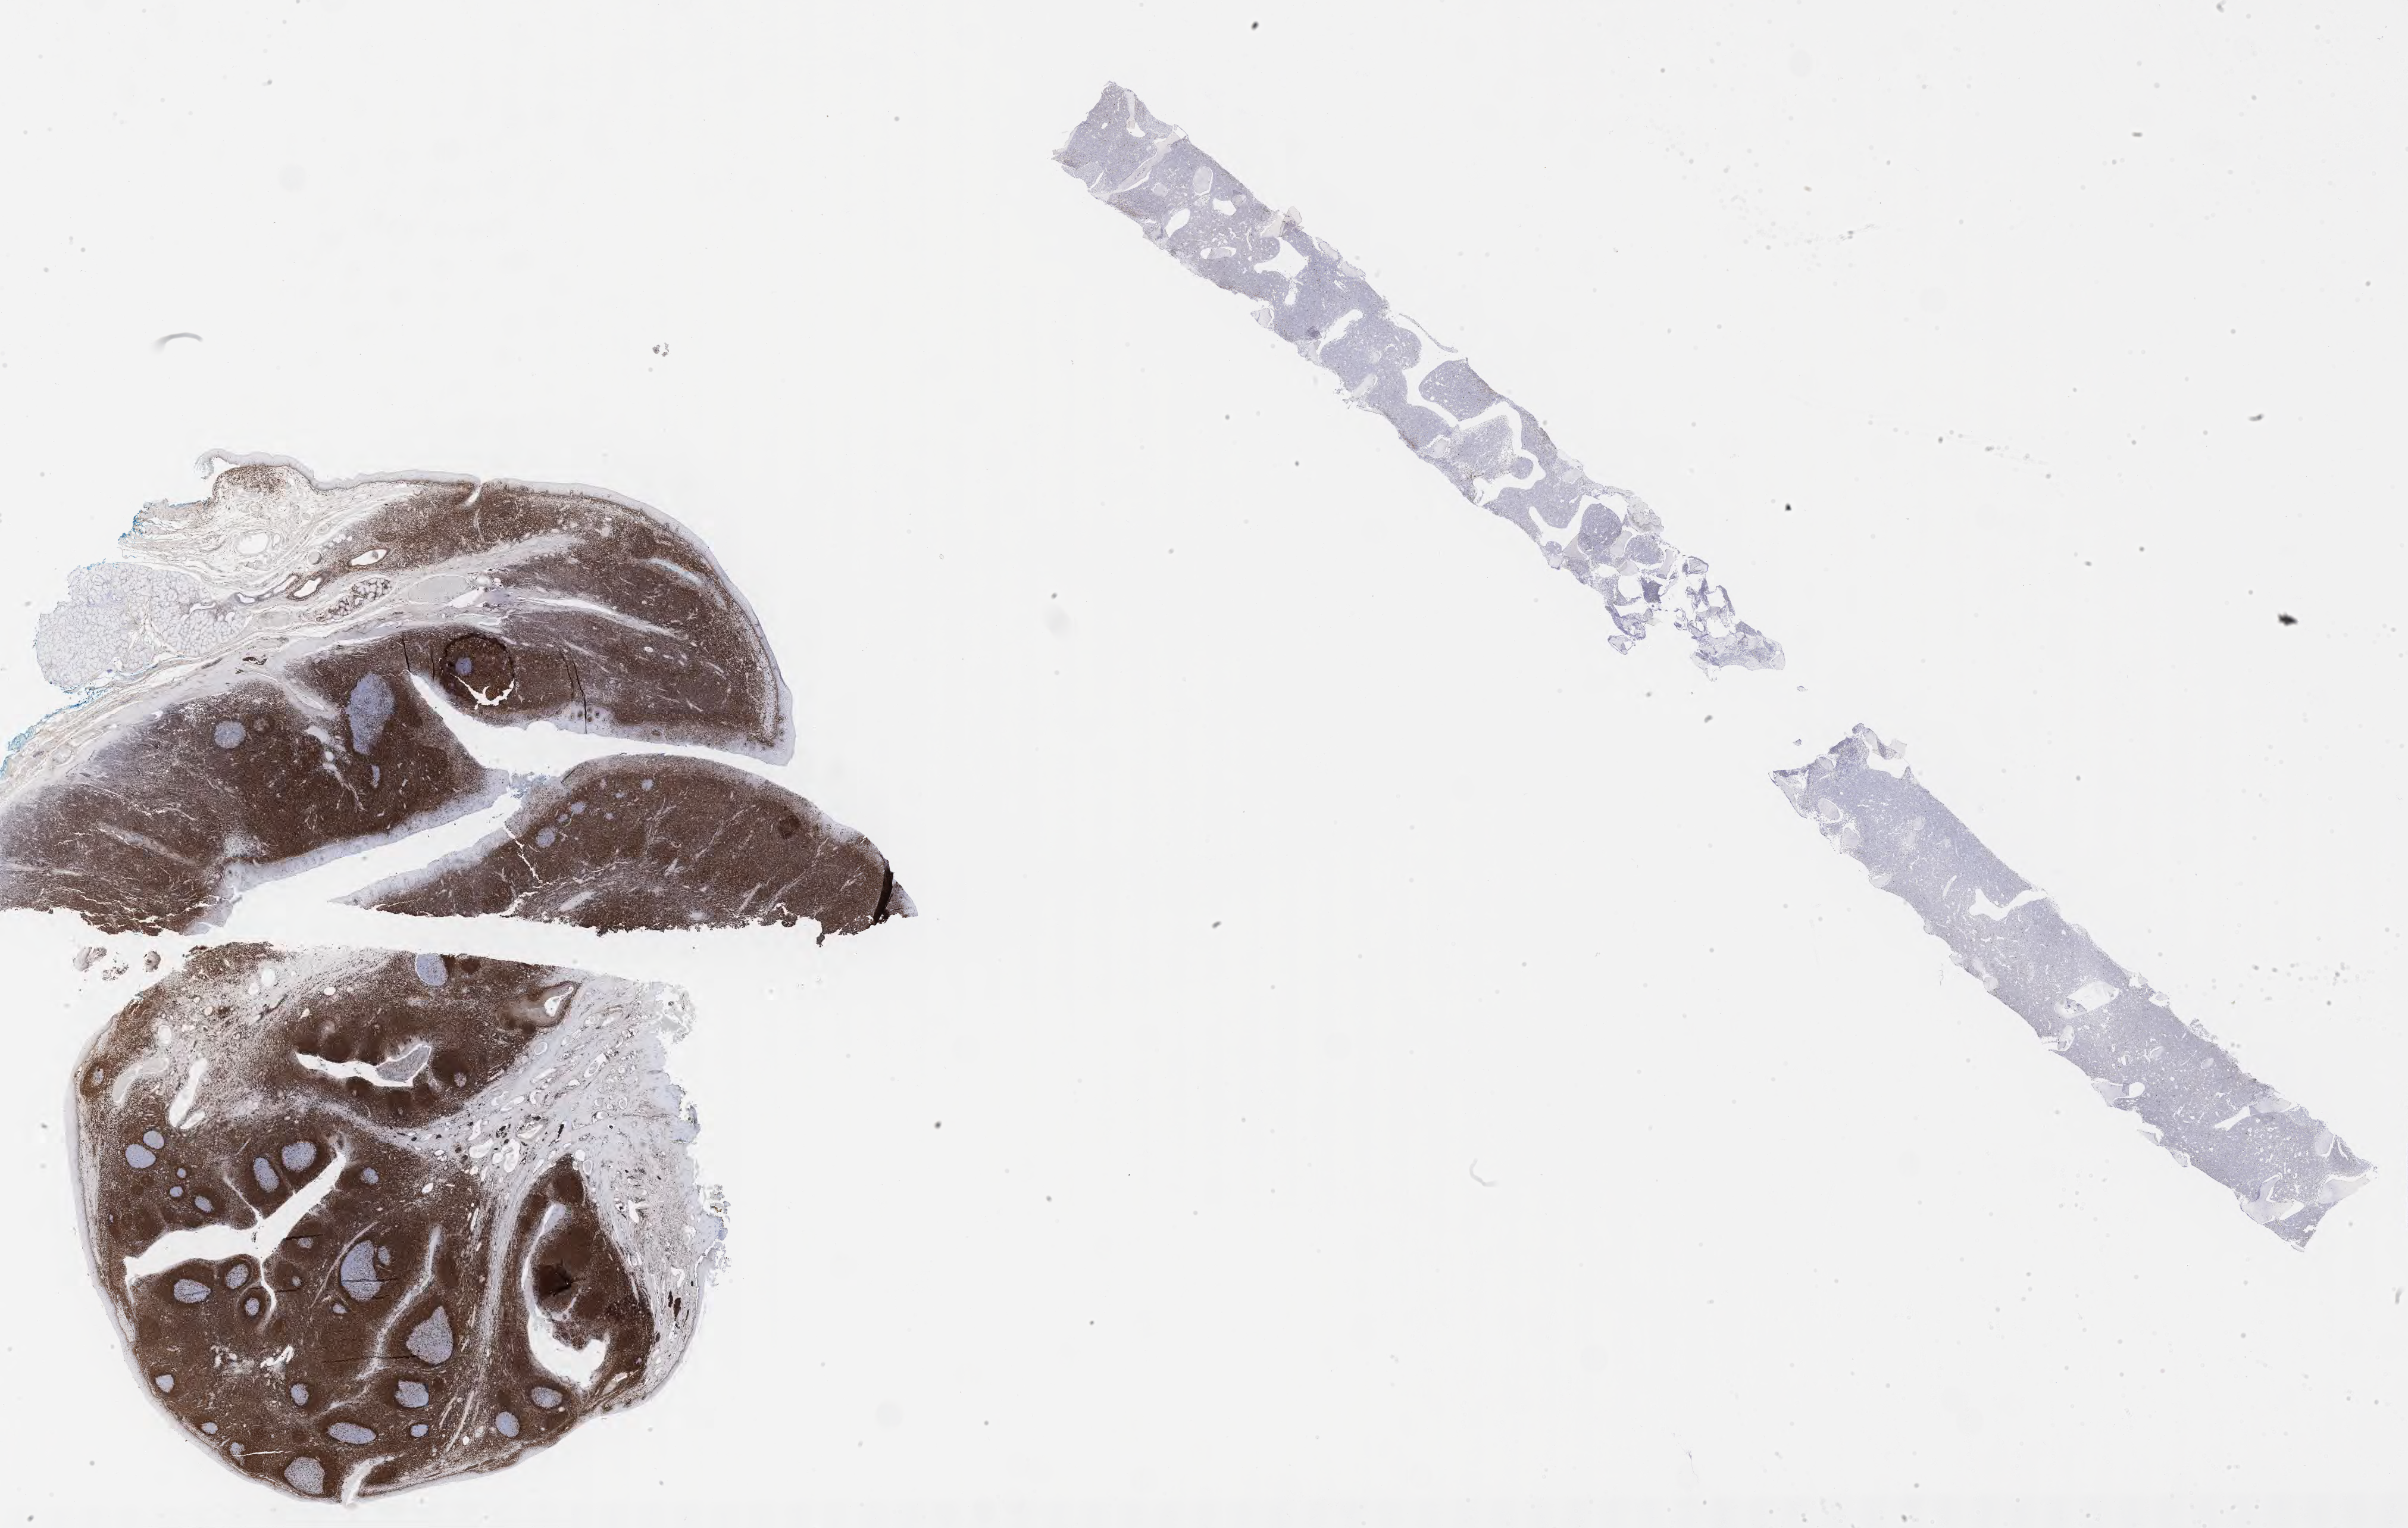
Whole-slide image, immunohistochemical stain for BCL2, shown as a low-resolution overview of the whole scanned area (about 32.7 x 20.8 mm). Tumor tissue. Male, age 7 years at initial diagnosis.
• histologic diagnosis: Burkitt lymphoma, NOS